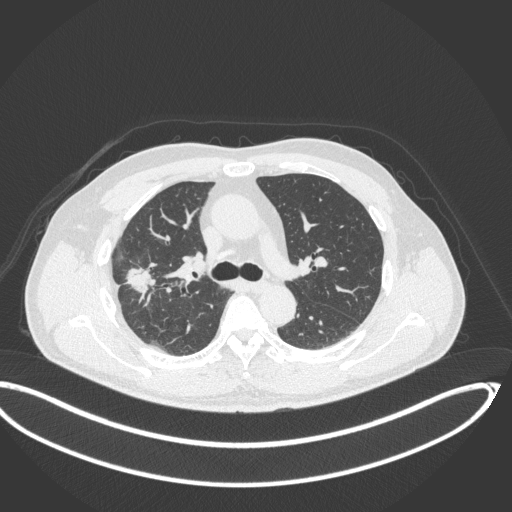
Chest CT, one axial slice; slice 223 of 341 in the series (ordered by position); reconstruction kernel B31f; lung window (W 1500 / L -600 HU); 512 × 512 image matrix, field of view 439 × 439 mm. Patient: male, 63 years. From the clinical record (not read from this slice): clinical TNM (as recorded): T1c N0 M0; histopathological grade: G2-3.
Structures marked on this image (rectangle marked by the reading radiologist):
- lung tumour (recorded histology: adenocarcinoma): box from (x=119, y=258) to (x=165, y=306) px